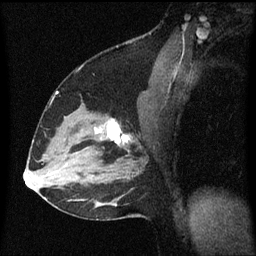
Breast MRI (dynamic contrast-enhanced), one sagittal slice; position 38 of 60 along the scan axis; dynamic contrast-enhanced series, image 2 of 3 at this slice position (ordered by acquisition); 1.5 T; TE 4.2 ms, TR 8.4 ms; 2 mm slice thickness; 256 × 256 image matrix, field of view 200 × 200 mm. Patient: female, 37 years. From the clinical record (not read from this slice): setting: breast cancer imaged before/during neoadjuvant chemotherapy; receptor status: HR-positive, HER2-negative.
Outlined on this slice (semi-automatic segmentation, software-assisted and operator-edited):
- analysis volume of interest (the breast-tissue region the enhancement analysis was run in; not a lesion): bounding box <94,114,134,157> (left, top, right, bottom; pixels)
- tumour enhancement mask (voxels above the 70 % enhancement threshold inside the analysis volume of interest): <95,120,130,145>